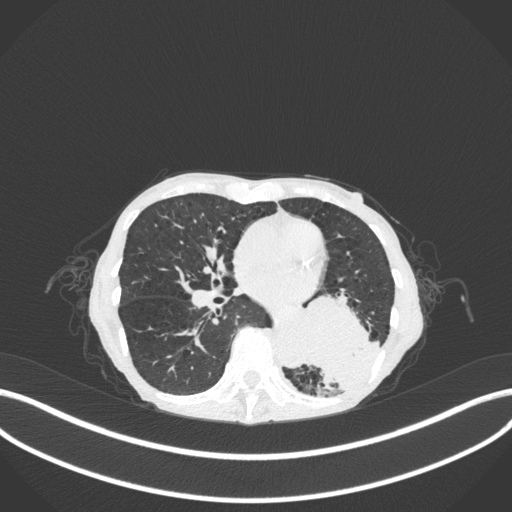
Chest CT, one axial slice; slice 126 of 347 in the series (ordered by position); reconstruction kernel B31f; 120 kVp; lung window (W 1500 / L -600 HU); 1 mm slice thickness; 512 × 512 image matrix, field of view 400 × 400 mm. Female patient, age 70 years. Case-level facts recorded for this patient, not image findings: clinical TNM (as recorded): T3 N0 M0; histopathological grade: G3.
Structures marked on this image (bounding box drawn by a radiologist):
- lung tumour (recorded histology: small cell carcinoma): bounding box [x1, y1, x2, y2] px = [292, 284, 380, 389]